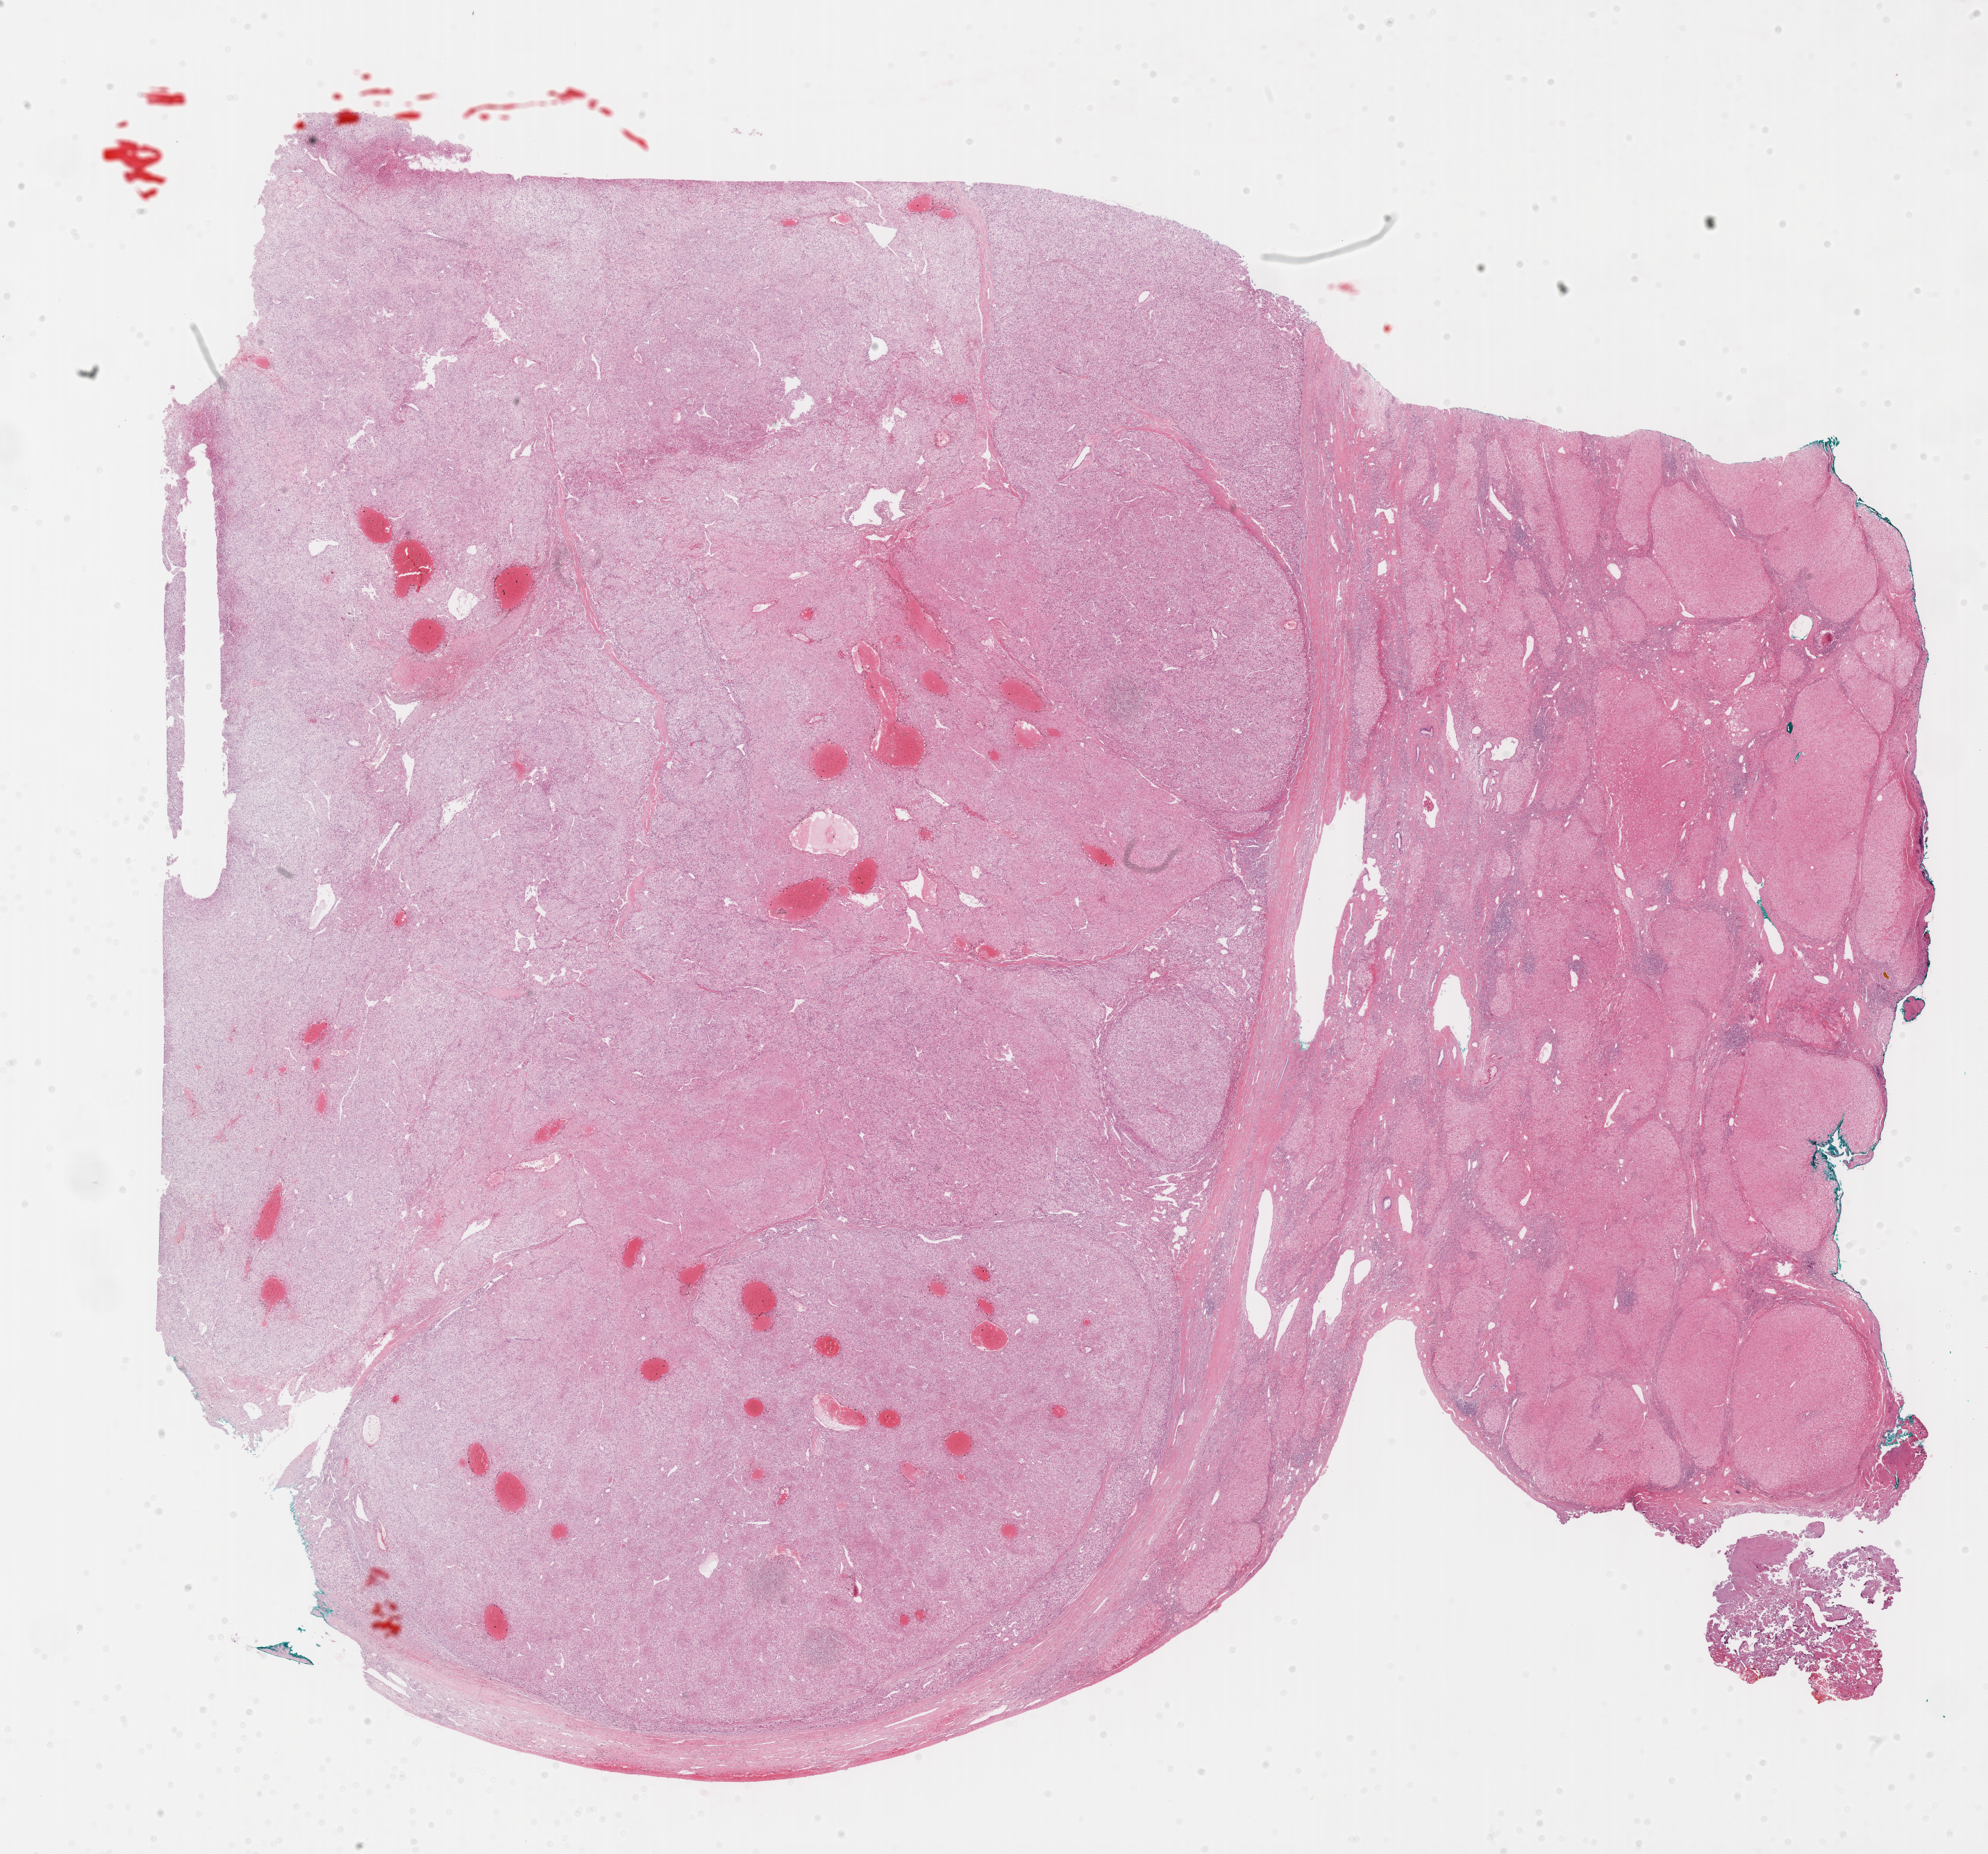
Digitized H&E tissue section (whole slide) — a low-resolution overview of the entire scanned area, about 23.1 x 21.6 mm (slide scanned at 40x), formalin-fixed paraffin-embedded (FFPE) diagnostic section, primary tumour sample from the liver. Patient: male, age at initial diagnosis 66 years. Histologic grade: G2 (moderately differentiated).
* pathologic diagnosis: Hepatocellular carcinoma, NOS
* AJCC pathologic stage: I (7th edition)